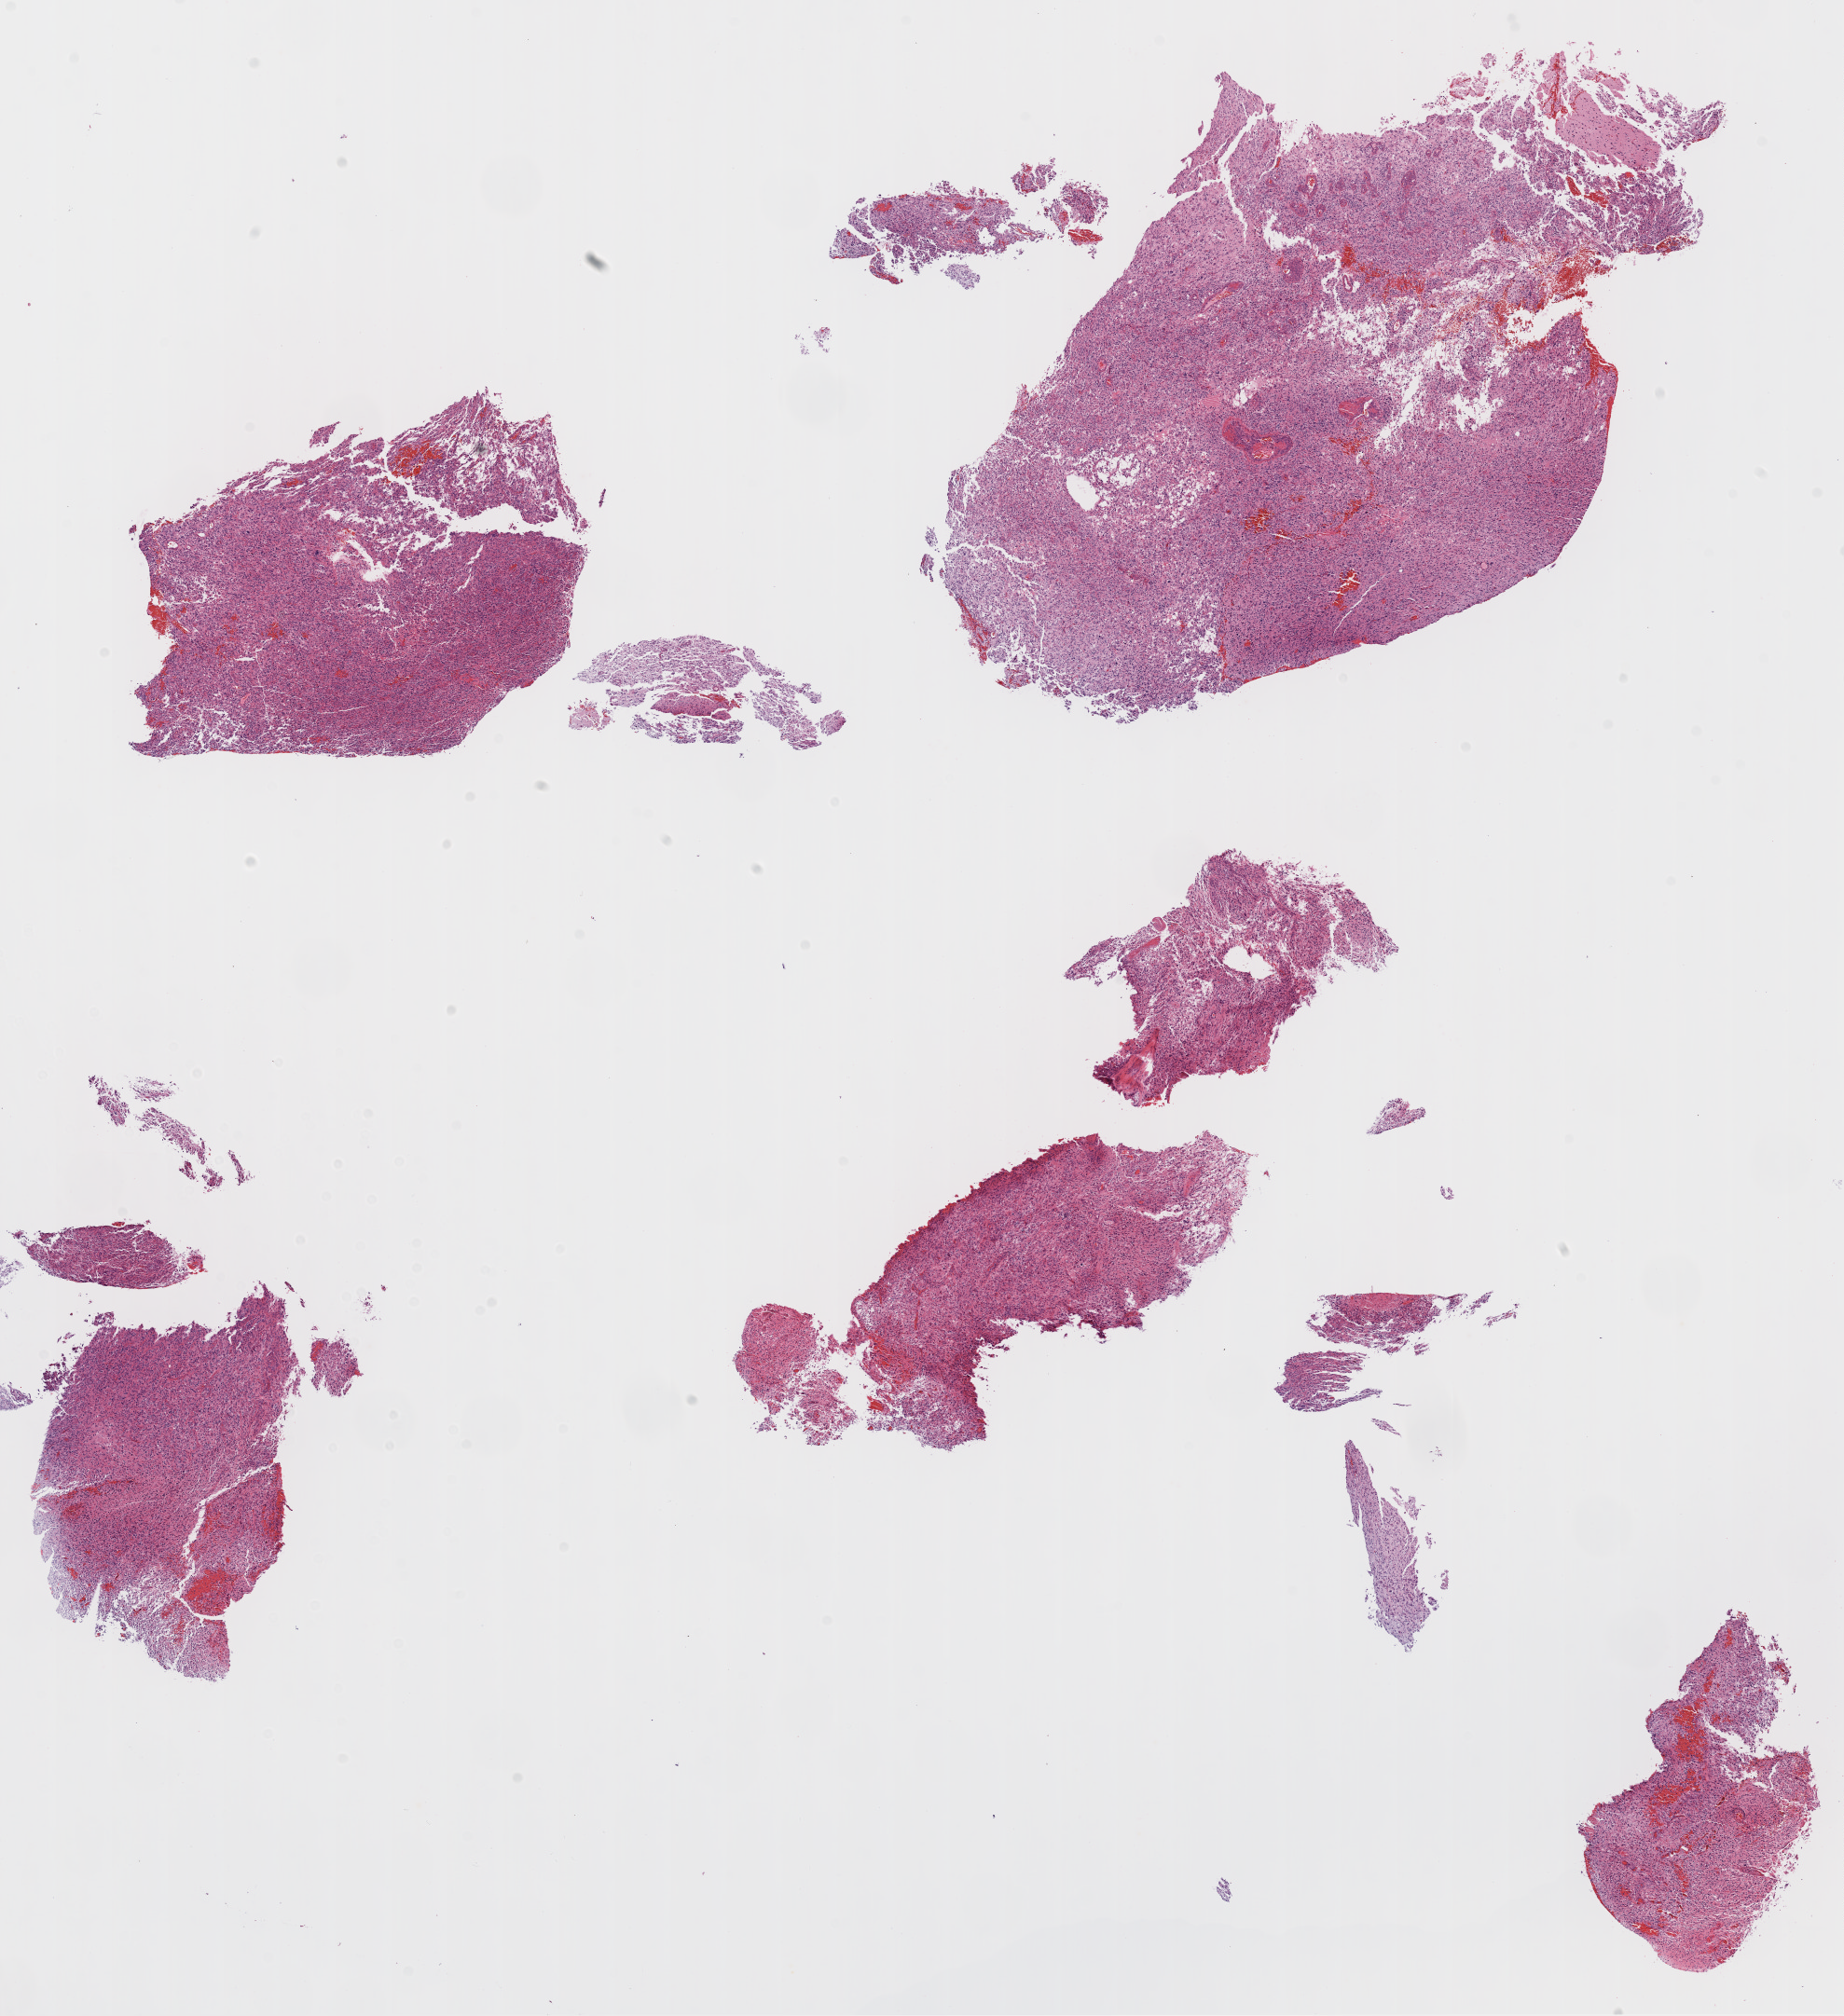
Digitized Hematoxylin and eosin (H&E) stained tissue section (whole slide) — low-resolution overview of the scanned area, about 16.0 x 17.4 mm. Formalin-fixed paraffin-embedded (FFPE) diagnostic section. Primary tumour sample from the brain. Patient: male, age at initial diagnosis 57 years.
Diagnosis: Glioblastoma.